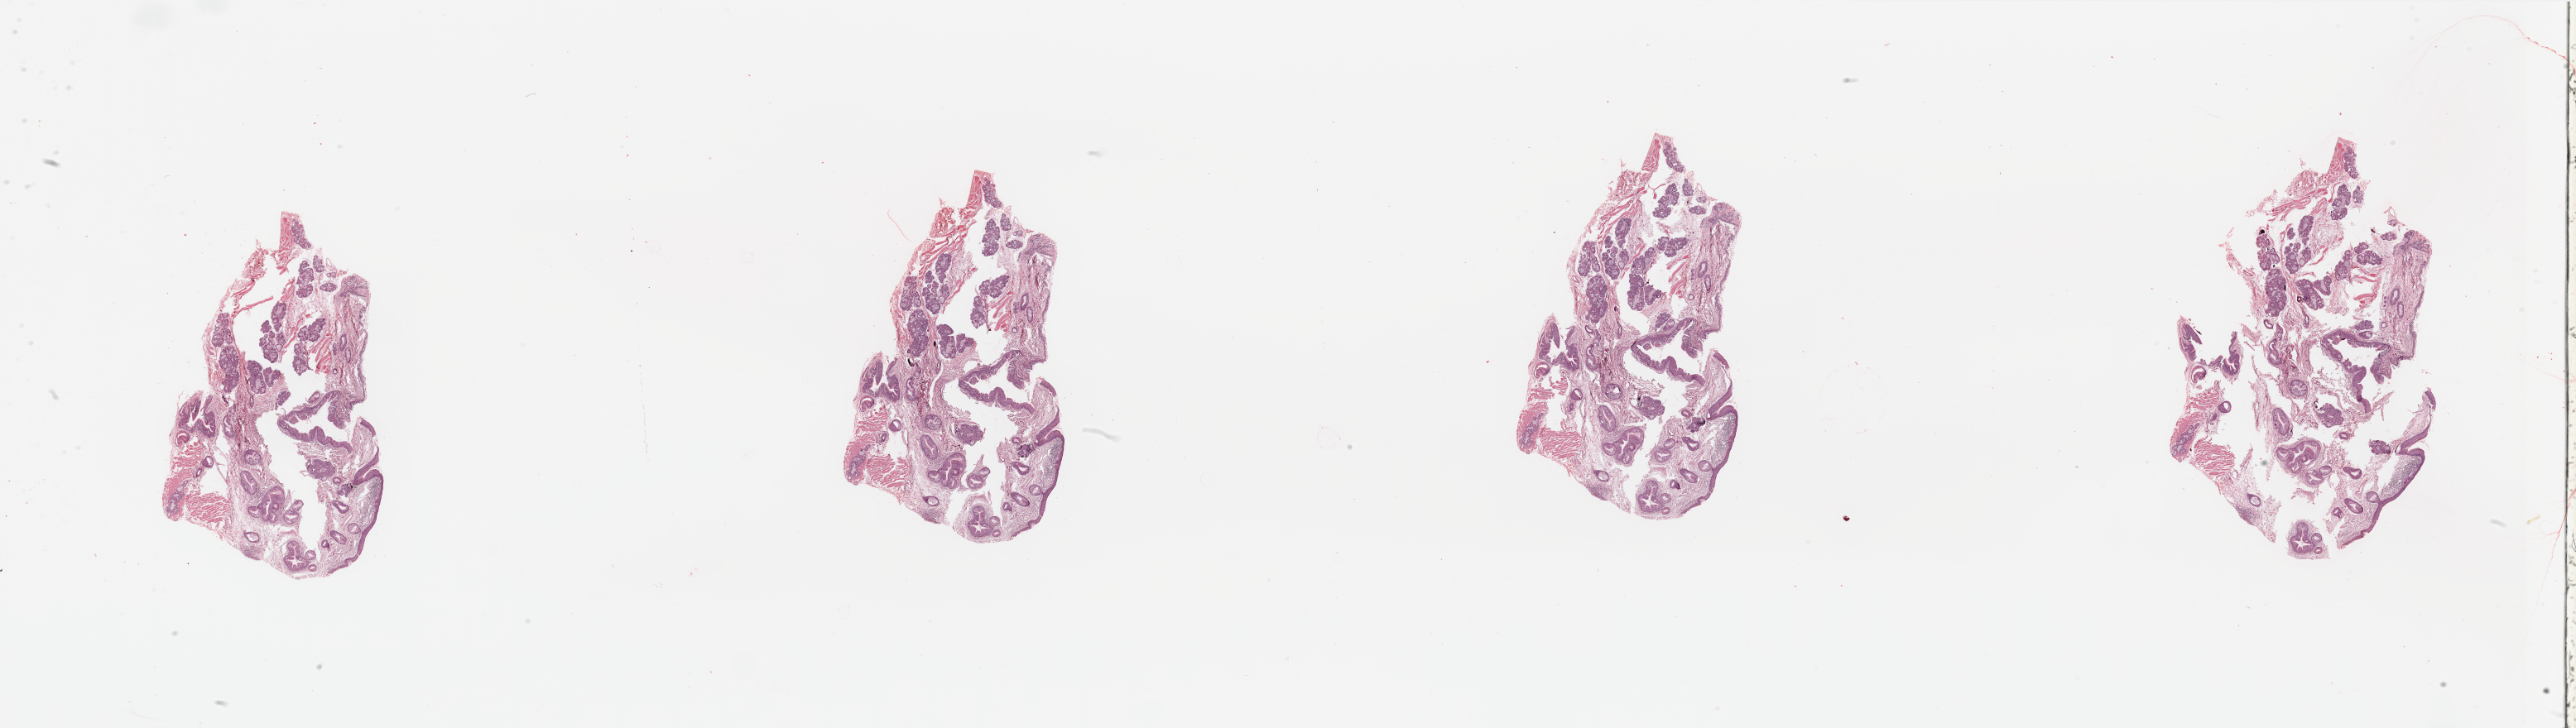
Digitized H&E-stained tissue section (whole slide) — a low-resolution overview of the entire scanned area, about 49.2 x 13.9 mm (from a 20x scan). Normal (non-tumour) tissue sample, sampled site: larynx. Male, 81 y/o.
• this section: normal (non-tumour) tissue from the same patient
• patient diagnosis: Squamous cell carcinoma, NOS